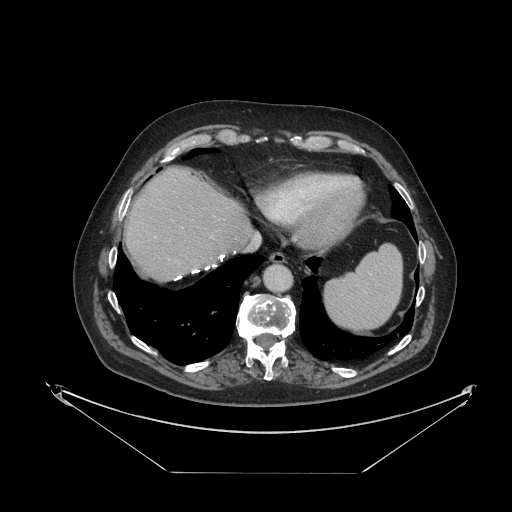
Contrast-enhanced abdominal CT, one axial slice. Slice 103 of 121 in the series (ordered by position). Reconstruction kernel STANDARD. 120 kVp. Soft-tissue window (W 400 / L 40 HU). 512 × 512 image matrix. Male patient, age 68 years. From the clinical record (not read from this slice): diagnosis: colorectal cancer liver metastases, imaged before liver resection; multiple liver metastases: no; largest metastasis: 4 cm; chemotherapy before resection: yes.
Structures marked on this image (manually delineated by an expert):
- liver: box from (x=126, y=169) to (x=251, y=280) px
- planned liver remnant (the part of the liver to remain after resection): (x=126, y=169)–(x=251, y=280)